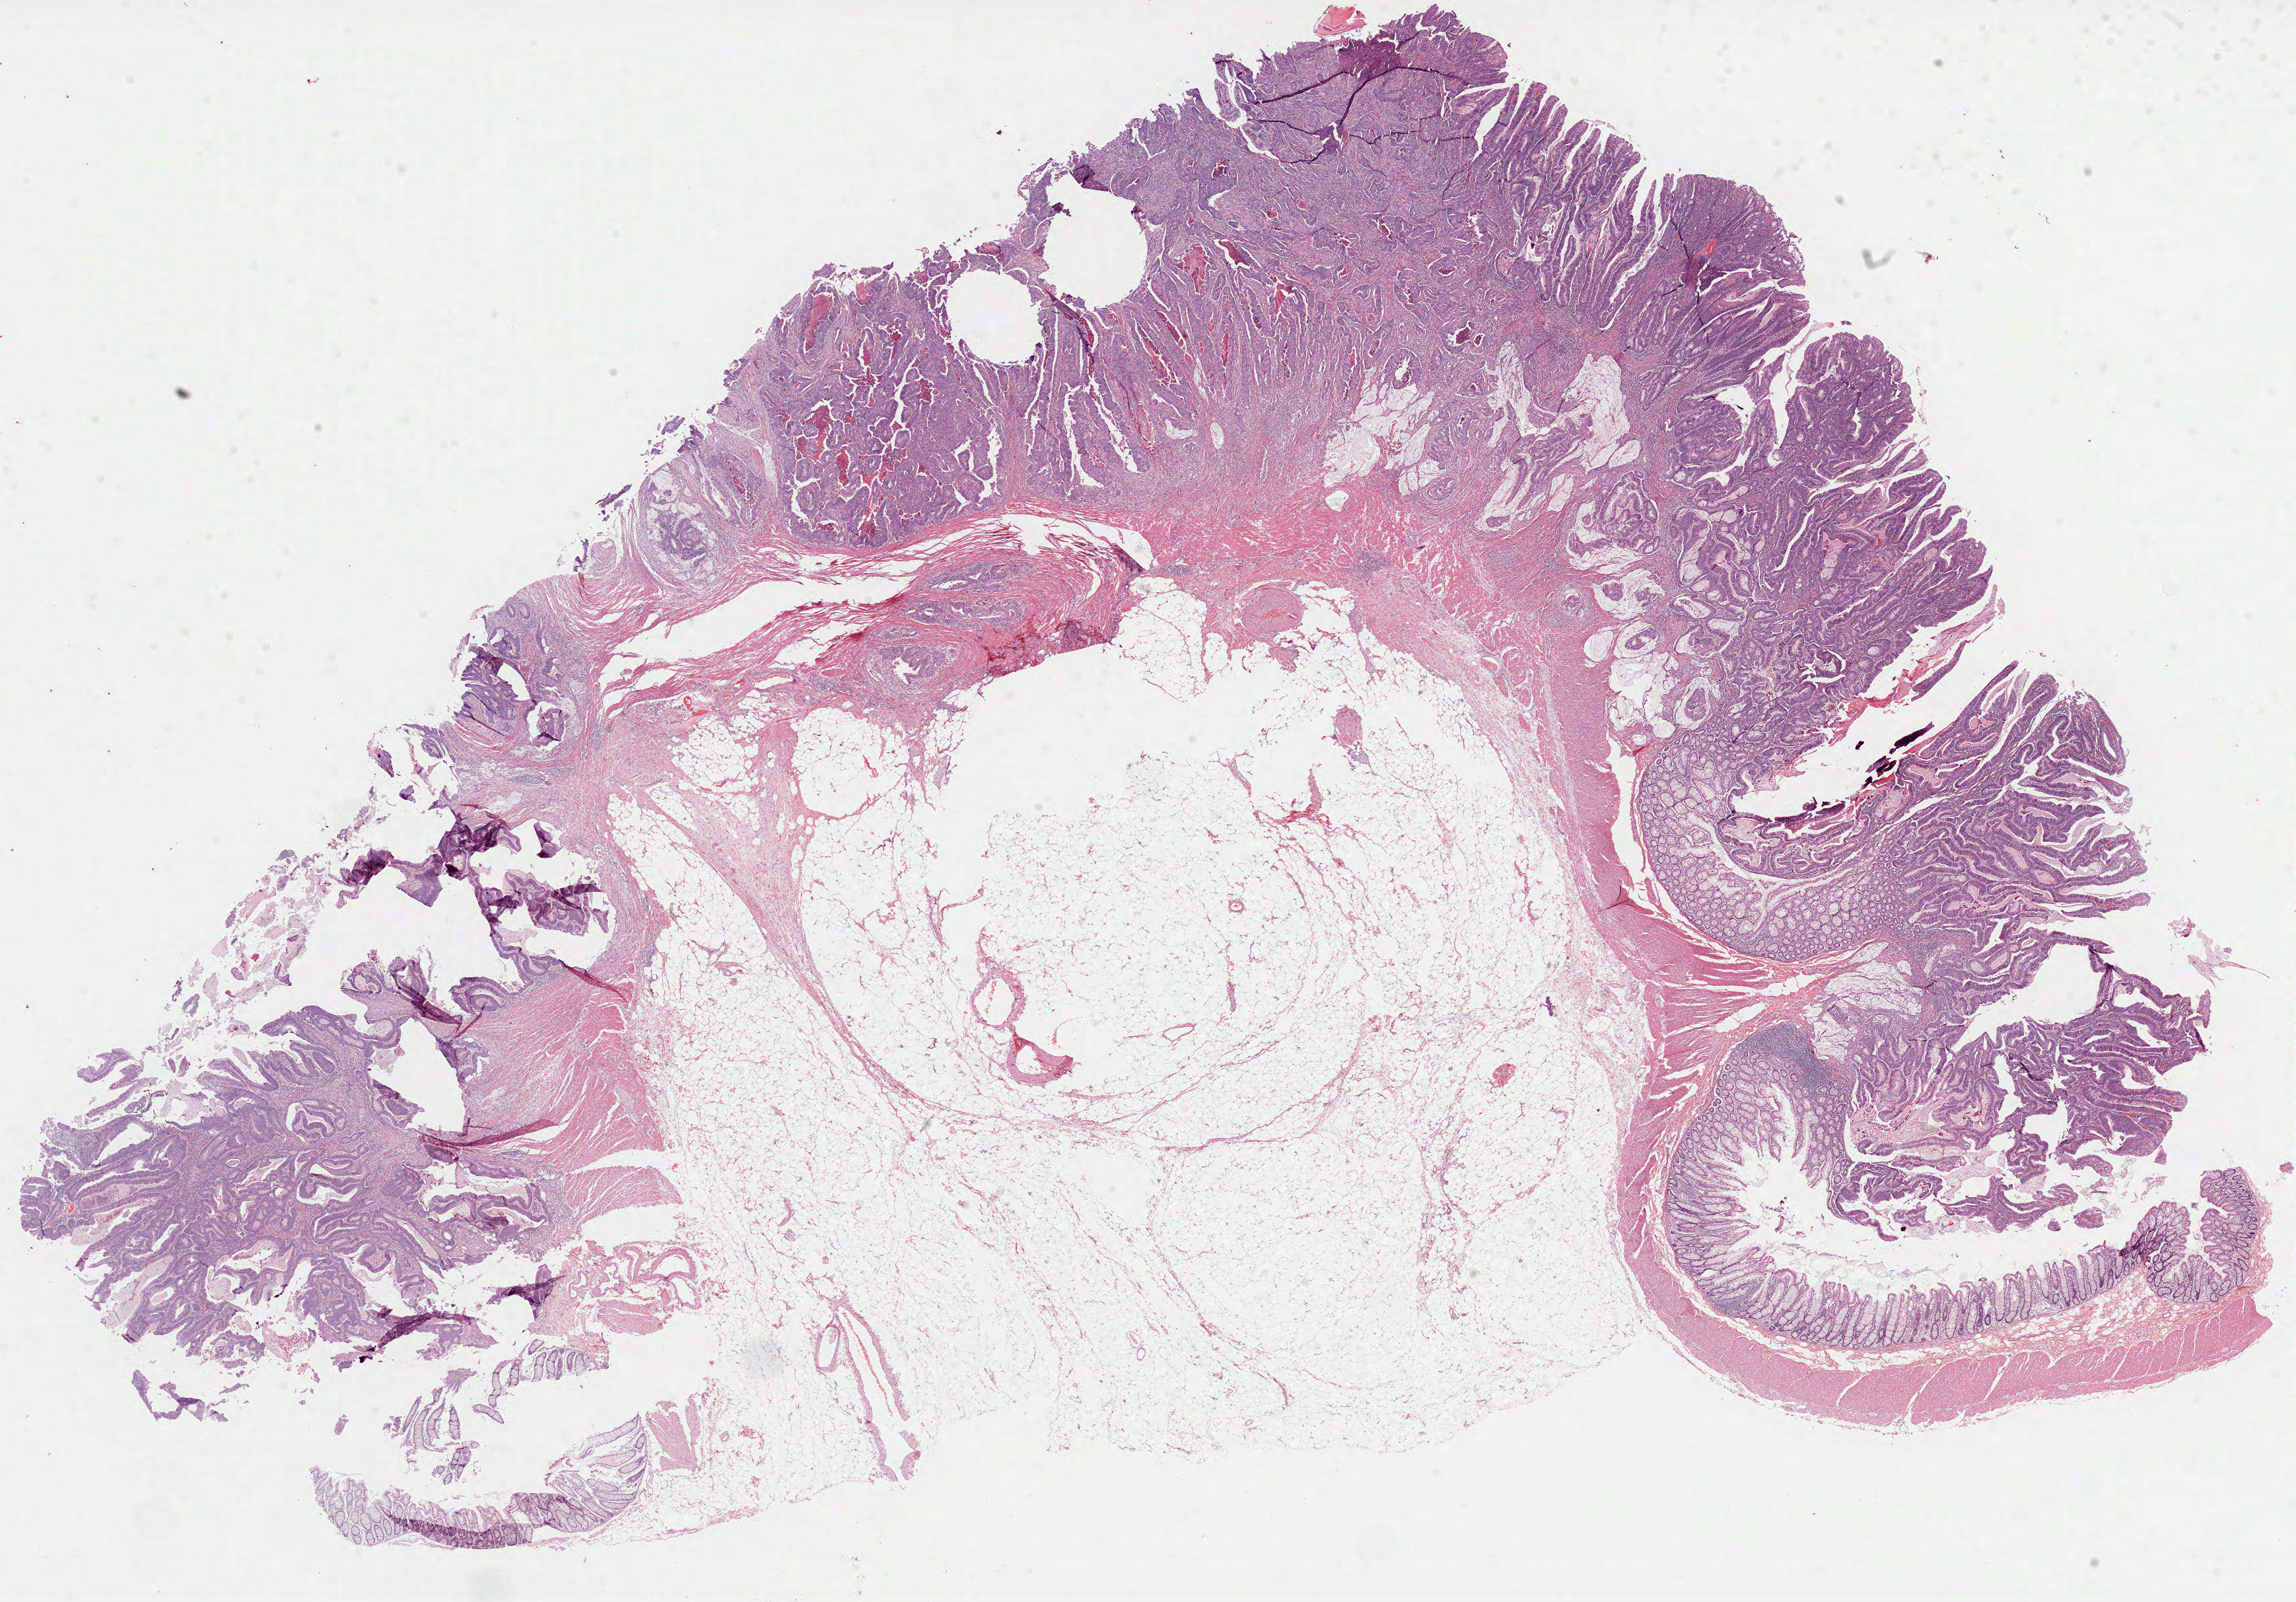
Digitized H&E-stained tissue section (whole slide) — a low-resolution overview of the entire scanned area, about 28.0 x 19.6 mm, formalin-fixed paraffin-embedded (FFPE) diagnostic section, sample: primary tumour, colon. Female patient; age at initial diagnosis 49 years.
Diagnosis: Adenocarcinoma, NOS (transverse colon). AJCC pathologic stage: III.